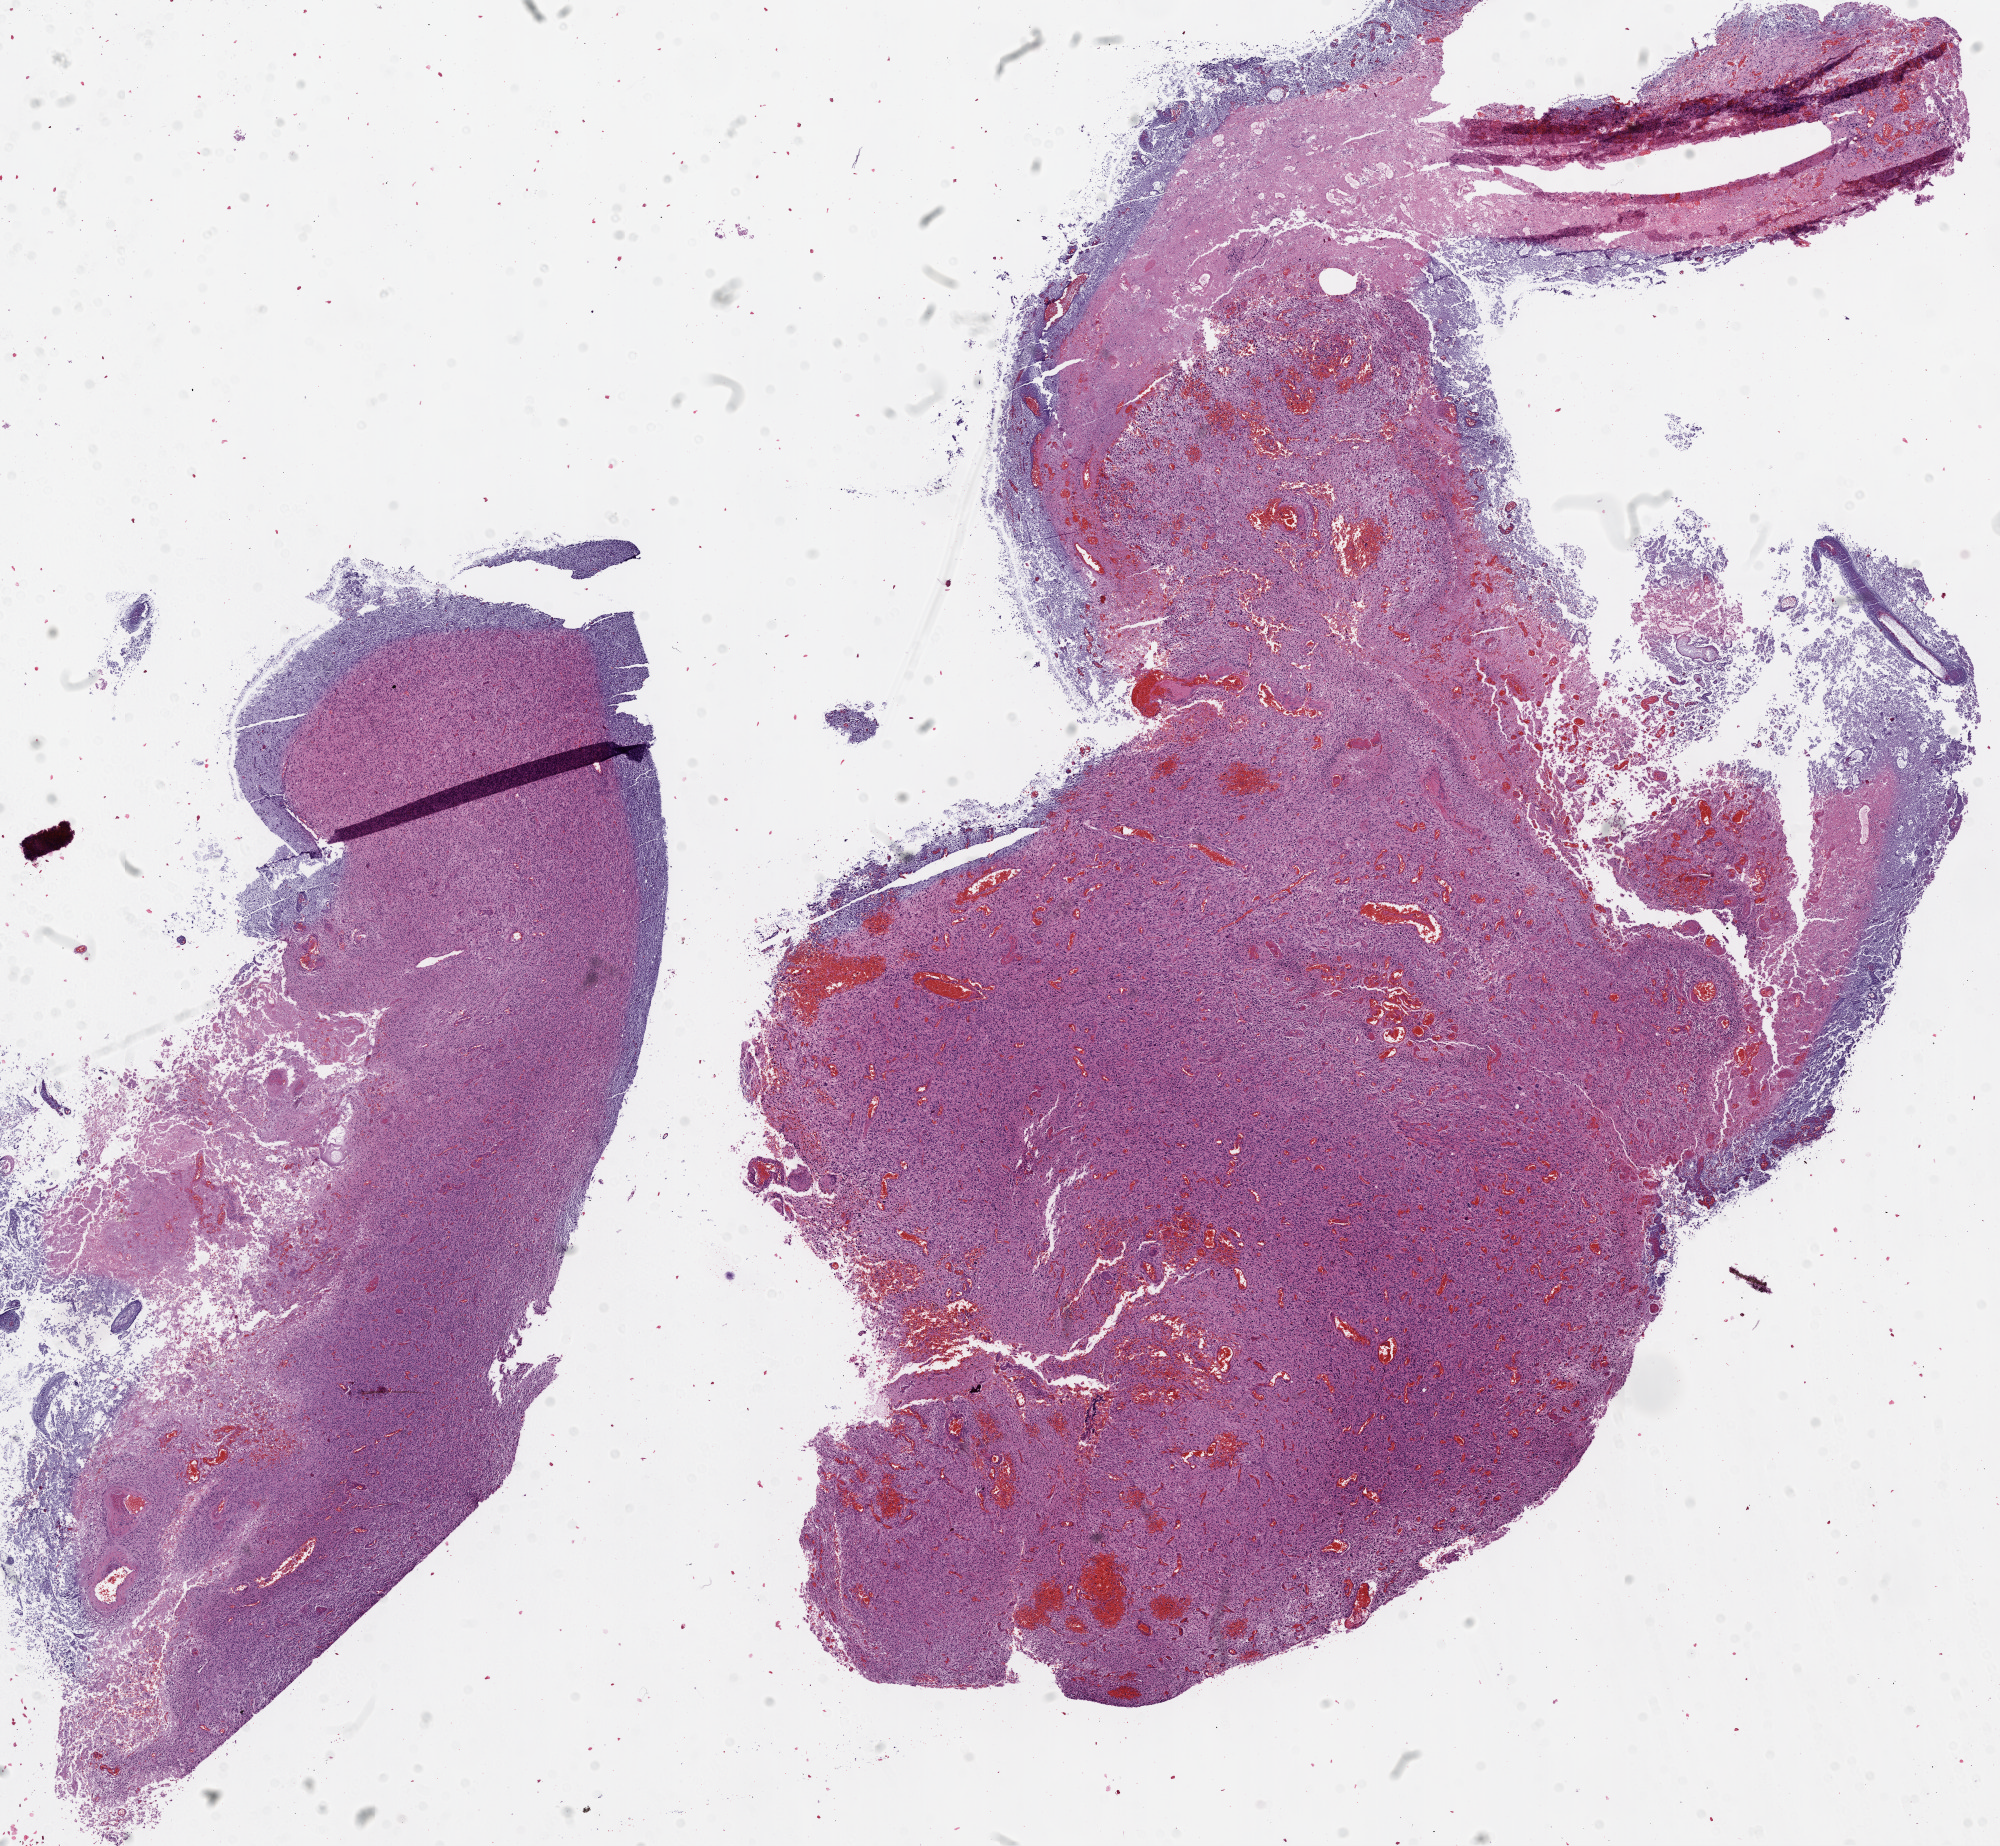
H&E whole-slide image, low-resolution overview of the scanned area, about 16.0 x 14.8 mm. Formalin-fixed paraffin-embedded (FFPE) diagnostic section. Brain, primary tumour sample. Female patient; age at initial diagnosis 50 years.
Histologic diagnosis: Glioblastoma.